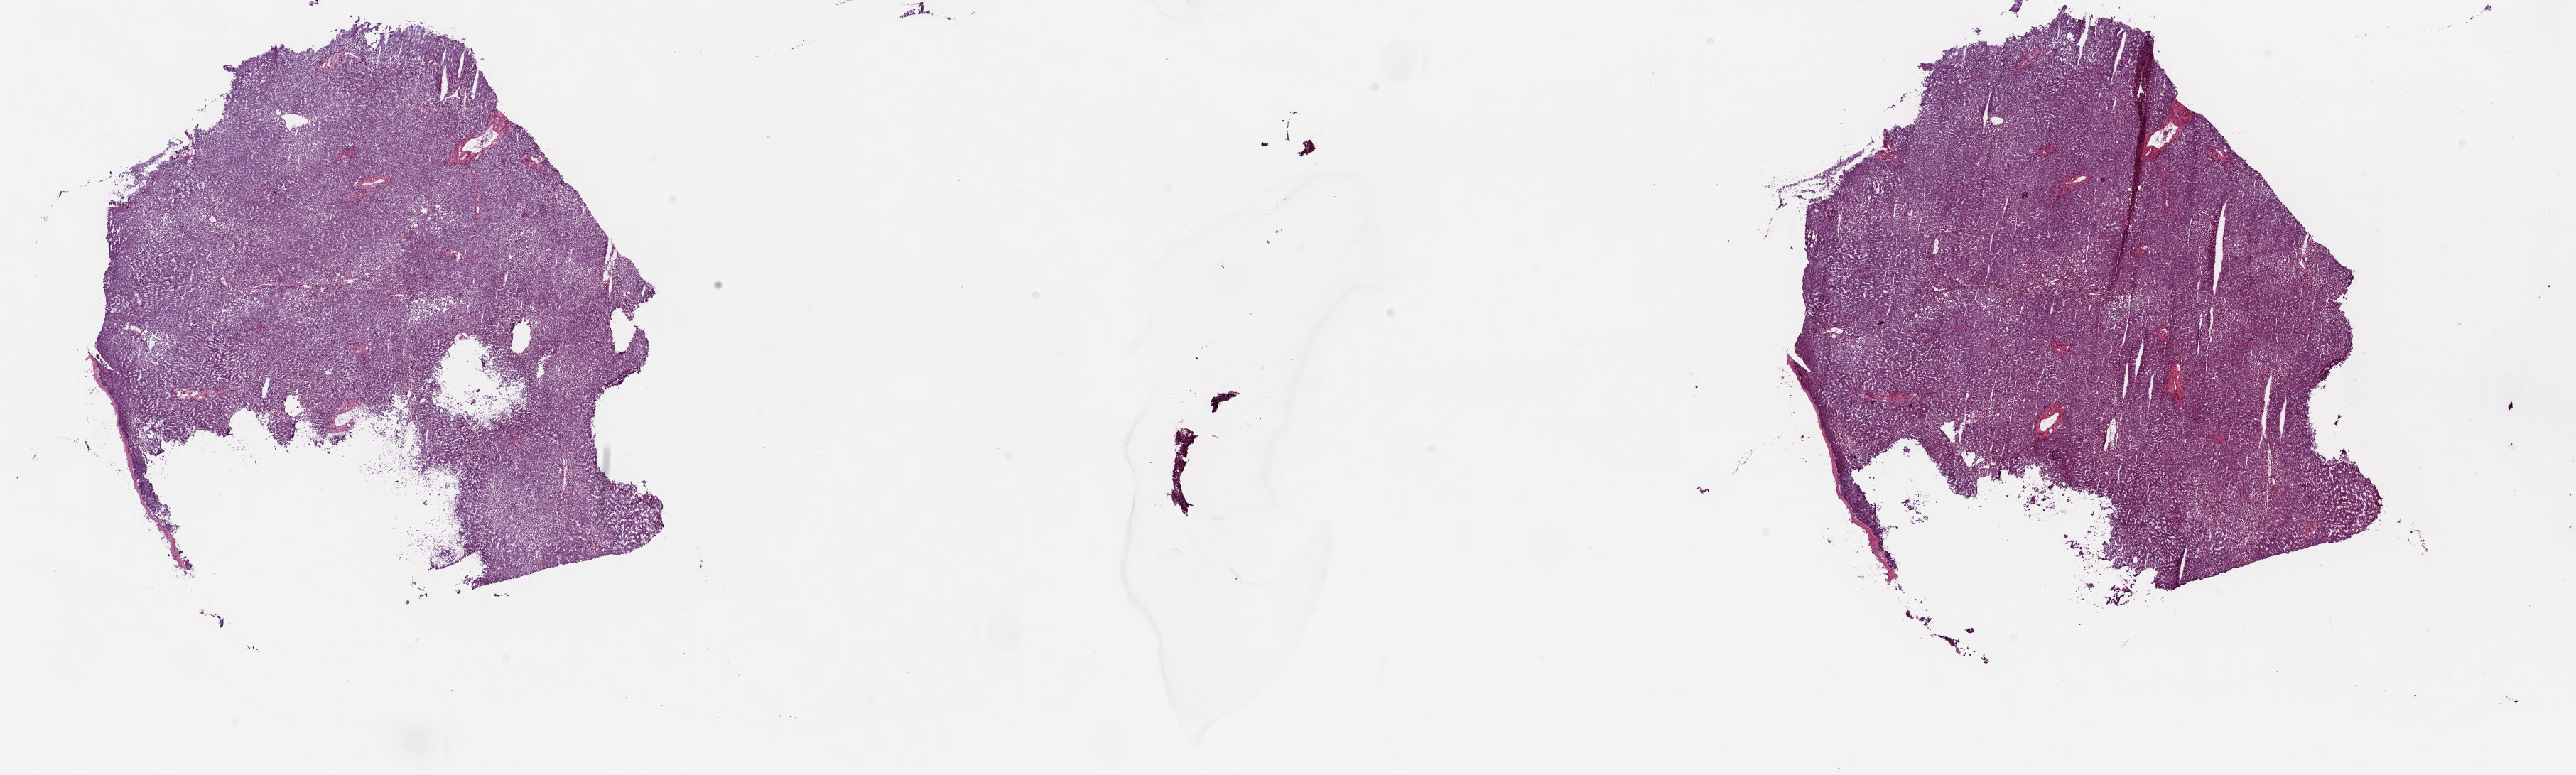
Whole-slide histology image, Hematoxylin and eosin (H&E) stained, whole scanned area (about 28.8 x 8.7 mm, from a 20x scan) shown as a low-resolution overview; frozen section from the top of the tissue portion; bile duct, solid tissue normal (non-tumour tissue) sample. Patient: male, age at initial diagnosis 71 years. Slide review estimates, as recorded: tumour cells 0%, tumour nuclei 0%, normal cells 100%, stromal cells 0%, necrosis 0%. Infiltration values recorded for this section: lymphocyte infiltration 2%, monocyte infiltration 0%, neutrophil infiltration 0%.
This section: solid tissue normal (non-tumour) sample from the same patient. Patient diagnosis: Cholangiocarcinoma (intrahepatic bile duct).